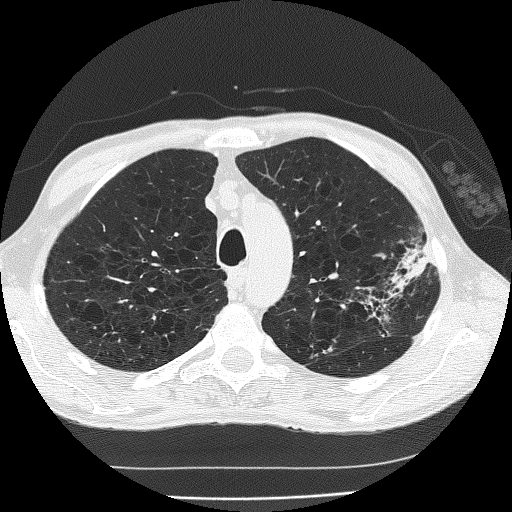
Chest CT (low-dose screening protocol), one axial image. Second annual screen. Lung window (W 1500 / L -600 HU). 2 mm slice thickness. Lung (sharp) reconstruction kernel (FC51). 120 kVp. Male participant, aged 60 years at enrolment.
Lesion marked by an expert reader, bounding box [x1, y1, x2, y2] px = [346, 244, 439, 337]. The screening reader recorded 2 non-calcified nodules or masses ≥4 mm on this exam; which of them this box marks is not recorded.